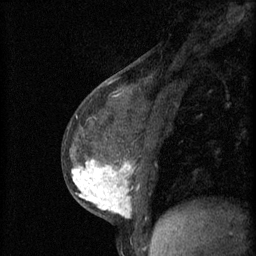
Breast MRI (dynamic contrast-enhanced), one sagittal slice. Position 25 of 60 along the scan axis. 3 images stored at this slice position (order not interpretable as contrast timing). 1.5 T. TE 4.2 ms, TR 11 ms. 256 × 256 image matrix. Female patient, age 37 years.
Structures marked on this image (semi-automatically segmented with operator editing):
- analysis volume of interest (the breast-tissue region the enhancement analysis was run in; not a lesion): bounding box <65,138,174,221> (left, top, right, bottom; pixels)
- tumour enhancement mask (voxels above the 70 % enhancement threshold inside the analysis volume of interest): <72,158,133,219>